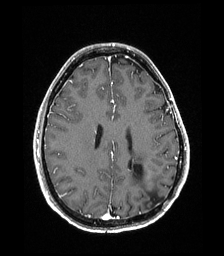
Brain MRI from a brain-tumour surgery series, one axial slice; slice 74 of 192 in the series (ordered by position); T1-weighted post-contrast; 1 mm slice thickness; 224 × 256 image matrix, field of view 224 × 256 mm. Case-level facts recorded for this patient, not image findings: histopathology: Low grade glioma; IDH mutation: no; tumour location: Left Parieto-Occipital Intraventricular.
Outlined on this slice (expert manual segmentation):
- previous resection cavity: bounding box <133,165,160,205> (left, top, right, bottom; pixels)
- tumour: <134,157,141,164>